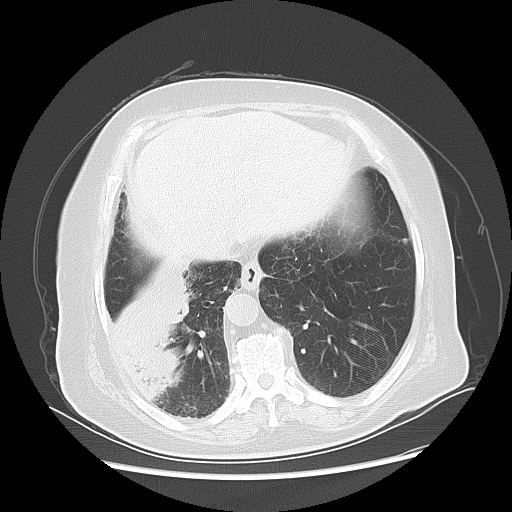
Chest CT, one axial slice. Slice 15 of 56 in the series (ordered by position). Reconstruction kernel LUNG. 120 kVp. Lung window (W 1500 / L -600 HU). 5 mm slice thickness. 512 × 512 image matrix, field of view 378 × 378 mm. Female patient, age 73 years. From the clinical record (not read from this slice): clinical TNM (as recorded): T3 N0 M0.
Annotated regions visible in this slice (bounding box drawn by a radiologist):
- lung tumour (recorded histology: adenocarcinoma): bounding box [x1, y1, x2, y2] px = [101, 270, 197, 403]